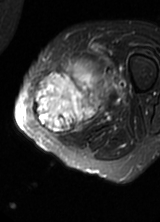
MRI of an extremity soft-tissue mass, one axial slice; T2-weighted fat-saturated; MR volume resampled by the dataset authors to the PET/CT grid (not the native acquisition matrix); 3.27 mm slice thickness; 160 × 222 image matrix, field of view 156 × 217 mm. Female patient. Case-level facts recorded for this patient, not image findings: histological type: pleomorphic leiomyosarcoma; grade: high; site of the primary tumour: left thigh.
Annotated regions visible in this slice (expert contour drawn on MRI and transferred to this co-registered scan by the dataset authors):
- gross tumour volume including surrounding oedema: bounding box [x1, y1, x2, y2] px = [34, 56, 117, 135]
- gross tumour volume (mass): [34, 75, 103, 135]